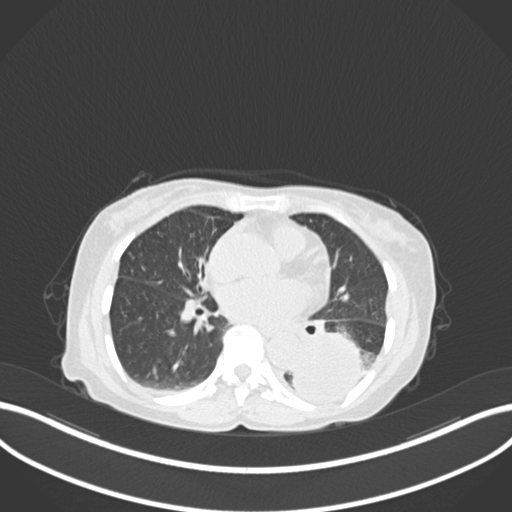
Chest CT, one axial slice. Slice 66 of 233 in the series (ordered by position). 120 kVp. Lung window (W 1500 / L -600 HU). 1 mm slice thickness. 512 × 512 image matrix. Patient: female, 78 years. From the clinical record (not read from this slice): clinical TNM (as recorded): T3 N0 M1.
Annotated regions visible in this slice (bounding box drawn by a radiologist):
- lung tumour (recorded histology: squamous cell carcinoma): bounding box [x1, y1, x2, y2] px = [287, 322, 369, 405]